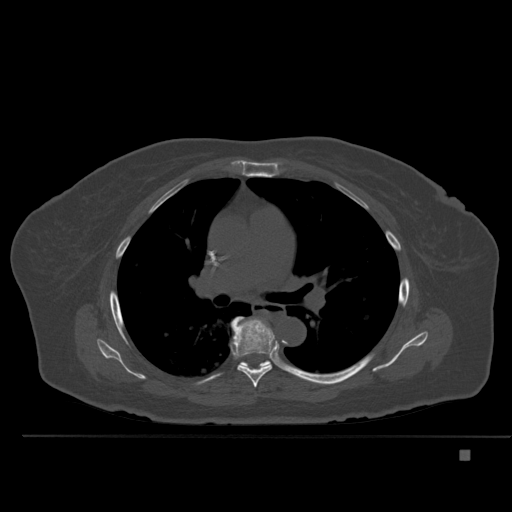
CT including the spine, one axial slice; bone window (W 1800 / L 400 HU); 512 × 512 image matrix. Patient: female, 74 years. From the clinical record (not read from this slice): primary cancer: colon.
Outlined on this slice (semi-automatically segmented with operator editing):
- T6 vertebra: bounding box (x1, y1, x2, y2) in pixels: (232, 318, 274, 388)
- T7 vertebra: (231, 317, 274, 370)